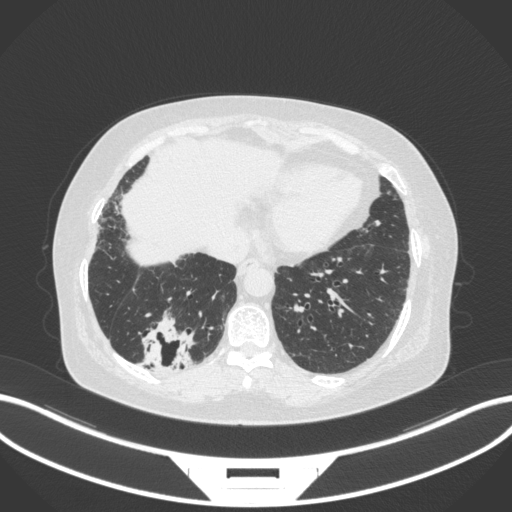
Chest CT, one axial slice. 120 kVp. Lung window (W 1500 / L -600 HU). 512 × 512 image matrix, field of view 400 × 400 mm. Patient: female, 65 years. Case-level facts recorded for this patient, not image findings: clinical TNM (as recorded): T2b N1 M0; histopathological grade: G1.
Annotated regions visible in this slice (bounding box drawn by a radiologist):
- lung tumour (recorded histology: adenocarcinoma): box from (x=133, y=311) to (x=196, y=373) px